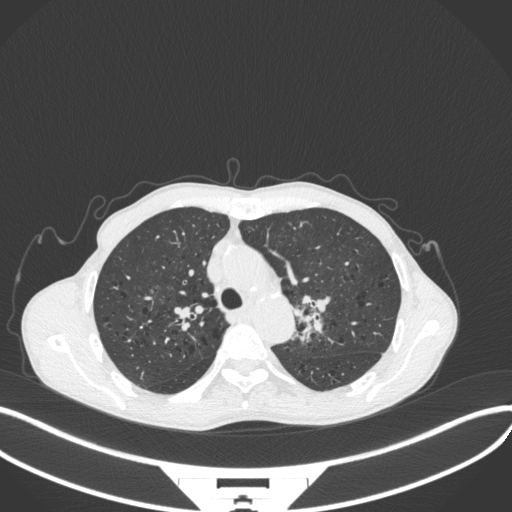
Chest CT, one axial slice; position 303 of 394 along the scan axis; reconstruction kernel B31f; lung window (W 1500 / L -600 HU); 1 mm slice thickness; 512 × 512 image matrix, field of view 400 × 400 mm. Patient: male, 65 years. Case-level facts recorded for this patient, not image findings: clinical TNM (as recorded): T2b N0 M0.
Outlined on this slice (rectangle marked by the reading radiologist):
- lung tumour (recorded histology: adenocarcinoma): bounding box <291,287,332,343> (left, top, right, bottom; pixels)